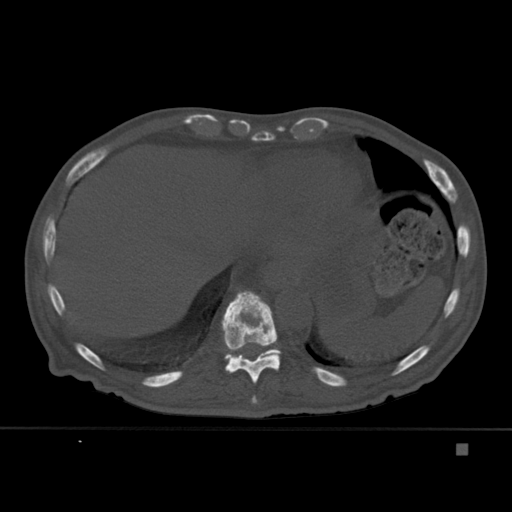
CT including the spine, one axial slice; position 231 of 451 along the scan axis; bone window (W 1800 / L 400 HU); 1.5 mm slice thickness; 512 × 512 image matrix, field of view 378 × 378 mm. Patient: male, 75 years. Case-level facts recorded for this patient, not image findings: primary cancer: prostate.
Structures marked on this image (semi-automatically segmented with operator editing):
- T10 vertebra: bounding box <221,291,280,384> (left, top, right, bottom; pixels)
- T11 vertebra: <224,348,281,361>
- T9 vertebra: <252,395,257,404>